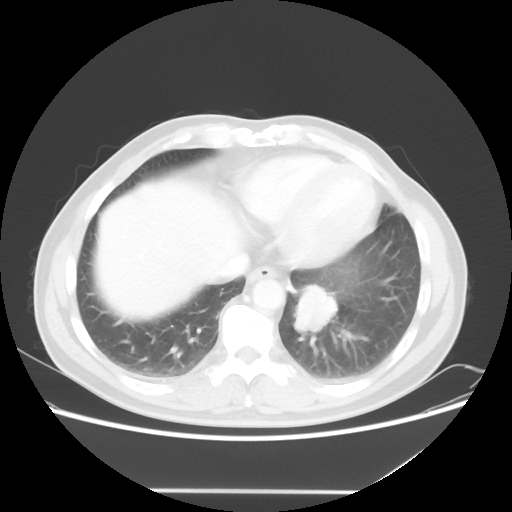
Chest CT, one axial slice; position 16 of 56 along the scan axis; lung window (W 1500 / L -600 HU); 5 mm slice thickness; 512 × 512 image matrix, field of view 385 × 385 mm. Patient: male, 61 years. Case-level facts recorded for this patient, not image findings: clinical TNM (as recorded): T1c N0 M0; histopathological grade: G3.
Structures marked on this image (rectangle marked by the reading radiologist):
- lung tumour (recorded histology: adenocarcinoma): box from (x=287, y=283) to (x=347, y=340) px